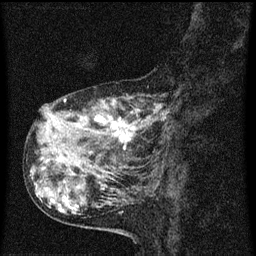
Breast MRI (dynamic contrast-enhanced), one sagittal slice. Dynamic contrast-enhanced series, image 2 of 3 at this slice position (ordered by acquisition). 1.5 T. TE 4.2 ms, TR 8 ms. 2 mm slice thickness. 256 × 256 image matrix. Female patient, age 55 years.
Annotated regions visible in this slice (semi-automatically segmented with operator editing):
- analysis volume of interest (the breast-tissue region the enhancement analysis was run in; not a lesion): bounding box [x1, y1, x2, y2] px = [38, 92, 175, 159]
- tumour enhancement mask (voxels above the 70 % enhancement threshold inside the analysis volume of interest): [44, 100, 165, 143]